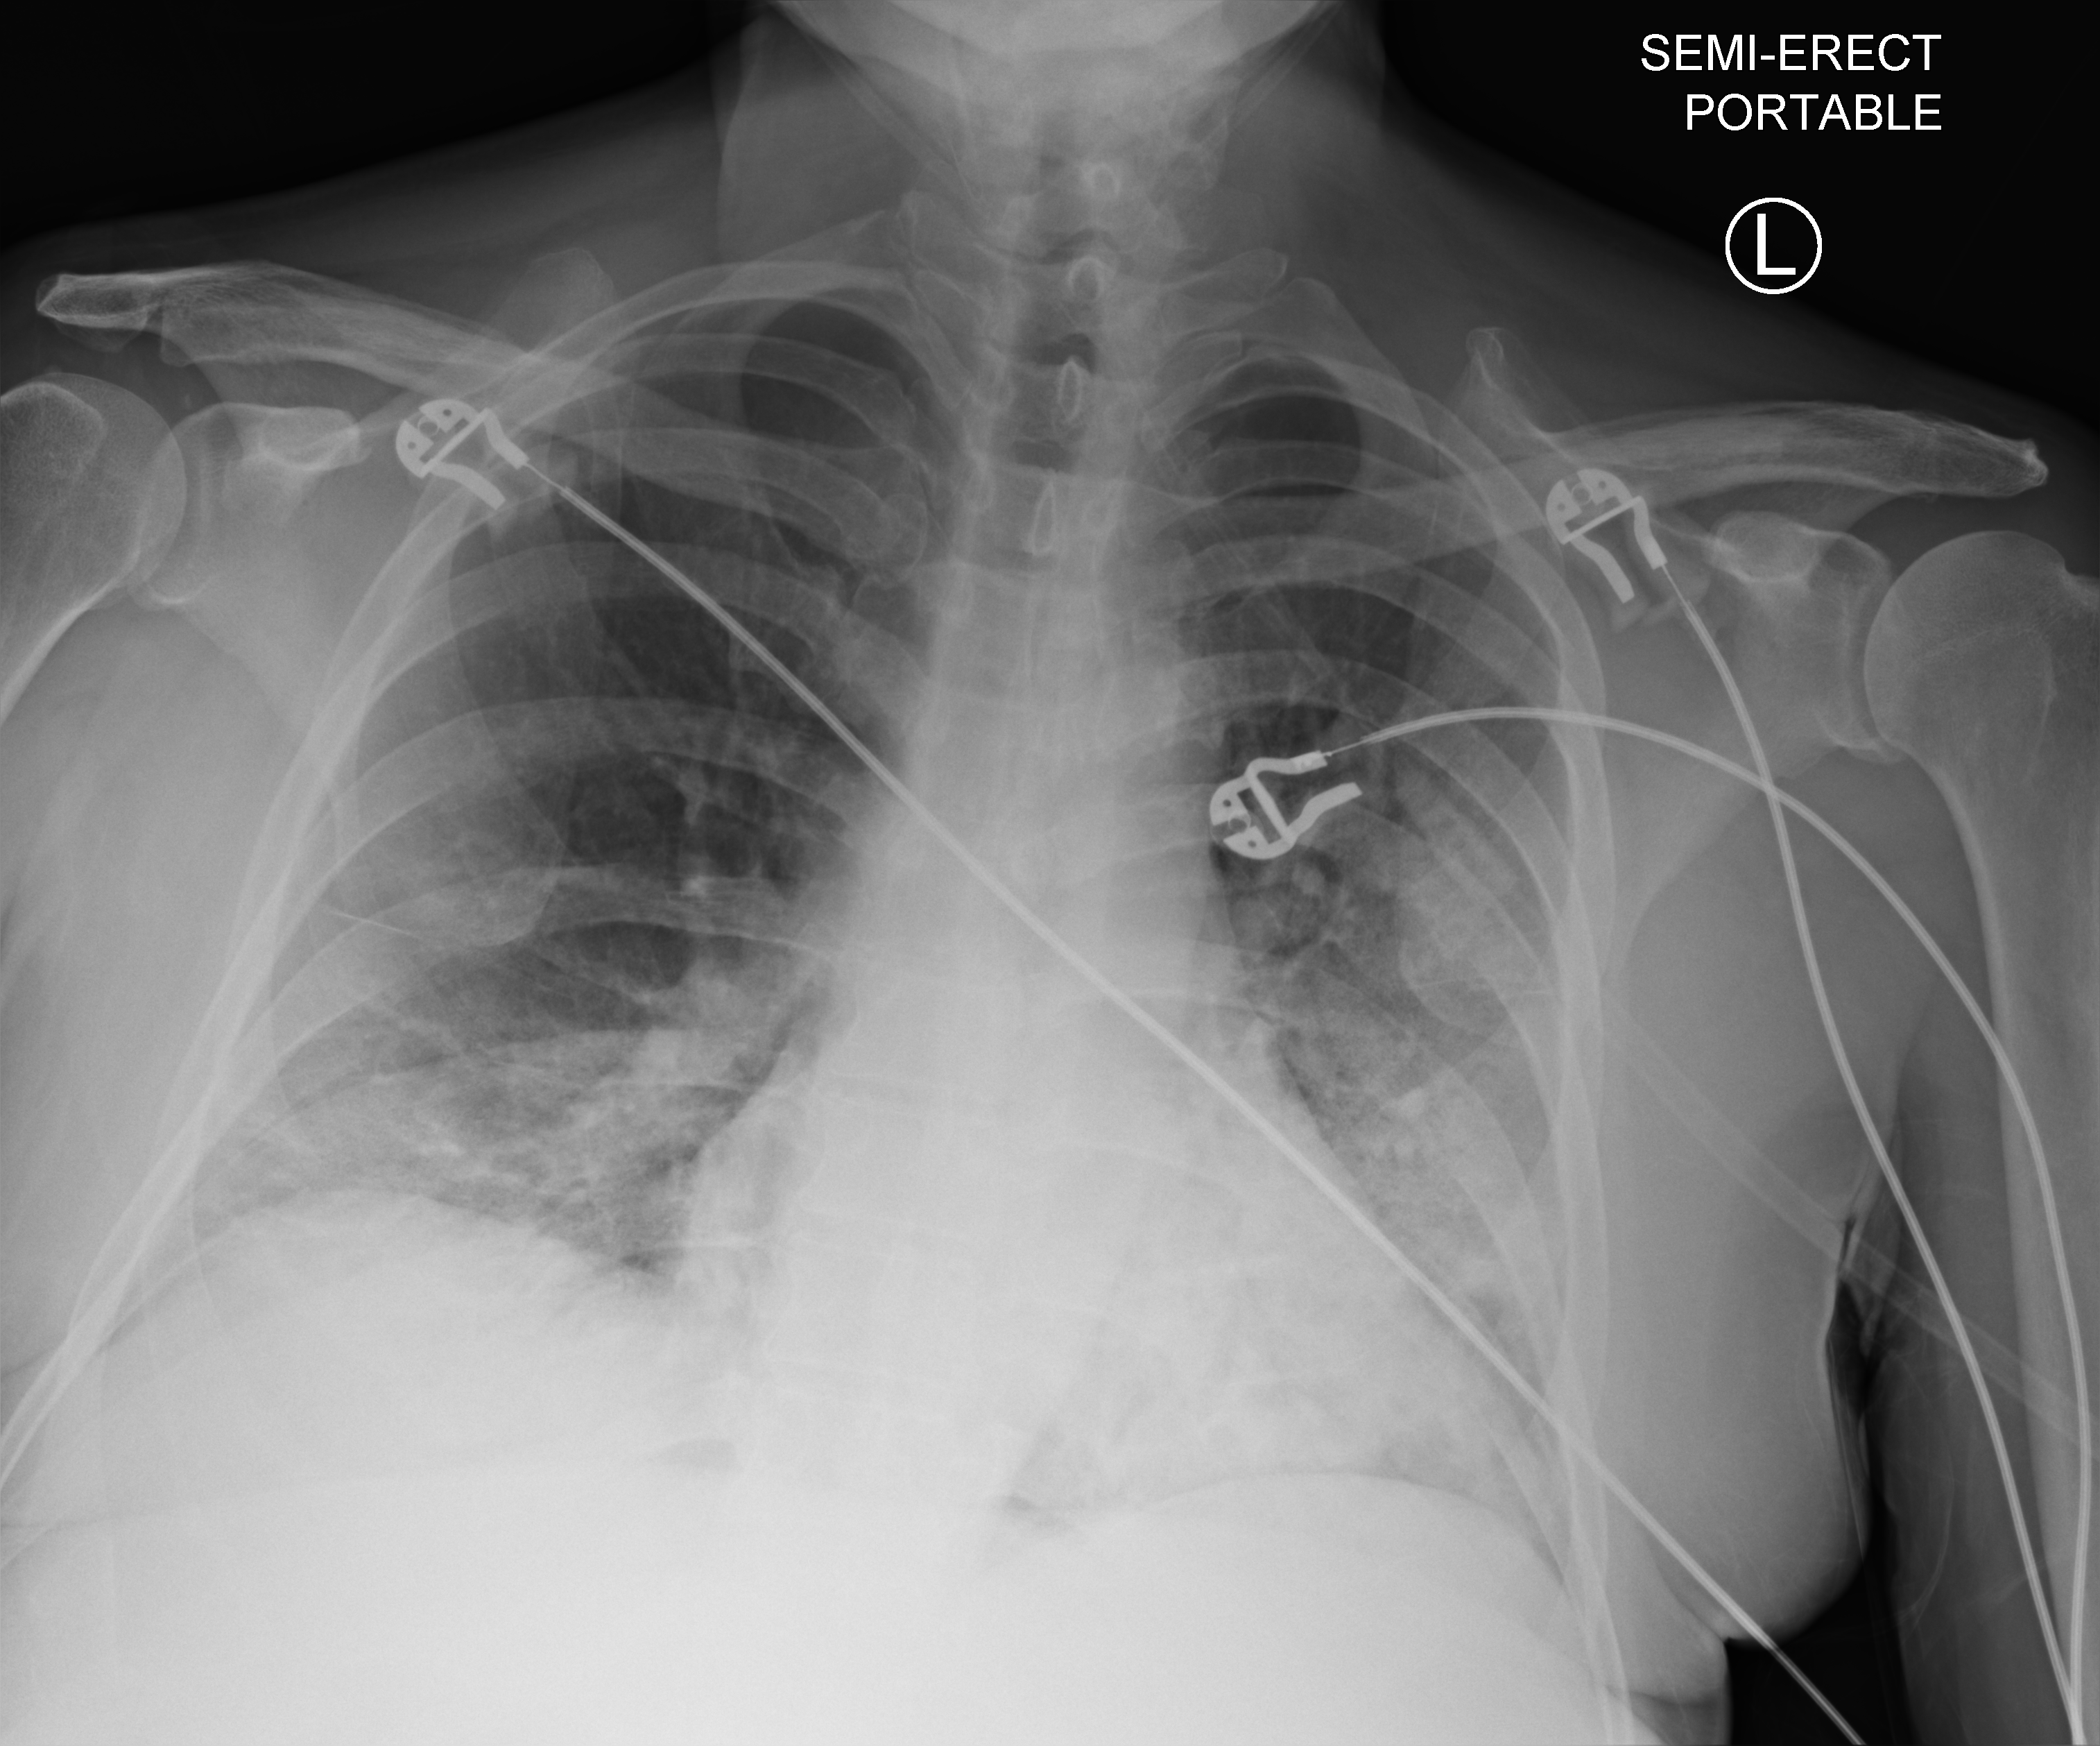
Portable chest radiograph, anteroposterior (AP) projection. Patient hospitalised with COVID-19; male, aged 60–74 years.
Hospital-stay facts (about this admission, not read from this image; timing relative to this image not recorded): length of hospital stay: 10 days; admitted to intensive care during this hospital stay: no.